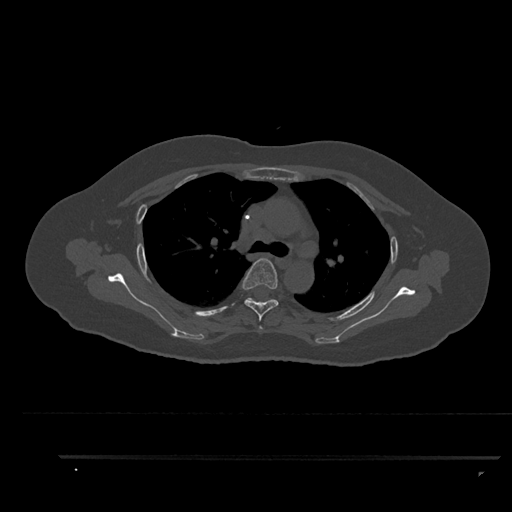
CT including the spine, one axial slice; slice 637 of 797 in the series (ordered by position); reconstruction kernel Br40s/3; 120 kVp; bone window (W 1800 / L 400 HU); 0.5 mm slice thickness; 512 × 512 image matrix, field of view 408 × 408 mm. Patient: female, 44 years. From the clinical record (not read from this slice): primary cancer: renal; vertebrae with lytic lesions (as recorded): L1.
Structures marked on this image (semi-automatic segmentation, software-assisted and operator-edited):
- T3 vertebra: bounding box (x1, y1, x2, y2) in pixels: (259, 326, 263, 329)
- T4 vertebra: (241, 258, 279, 321)
- T5 vertebra: (244, 298, 249, 302)